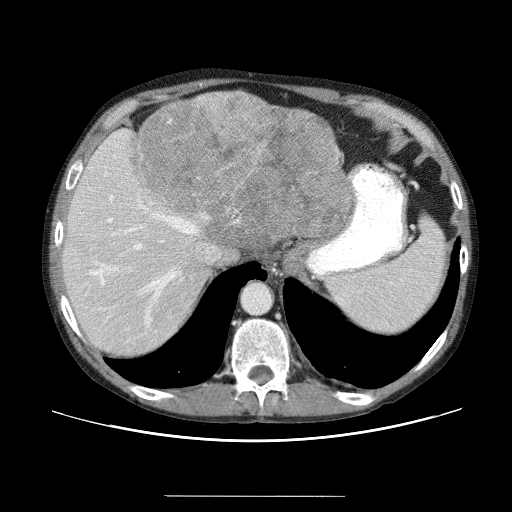
Contrast-enhanced abdominal CT (liver protocol), one axial slice. Slice 45 of 69 in the series (ordered by position). Soft-tissue window (W 400 / L 40 HU). 2.5 mm slice thickness. 512 × 512 image matrix, field of view 380 × 380 mm. From the clinical record (not read from this slice): diagnosis: hepatocellular carcinoma (patient treated with transarterial chemoembolisation; whether this scan precedes or follows treatment is not stated here); TNM stage (as recorded): Stage-IVB; Child-Pugh class: B; tumour nodularity: multinodular.
Outlined on this slice (semi-automatically segmented with operator editing):
- liver parenchyma outside the tumour (the mass and vessels are separate outlines, so this box may not span the whole liver): bounding box <60,104,340,360> (left, top, right, bottom; pixels)
- mass: <135,90,354,269>
- liver vessels: <82,148,187,341>